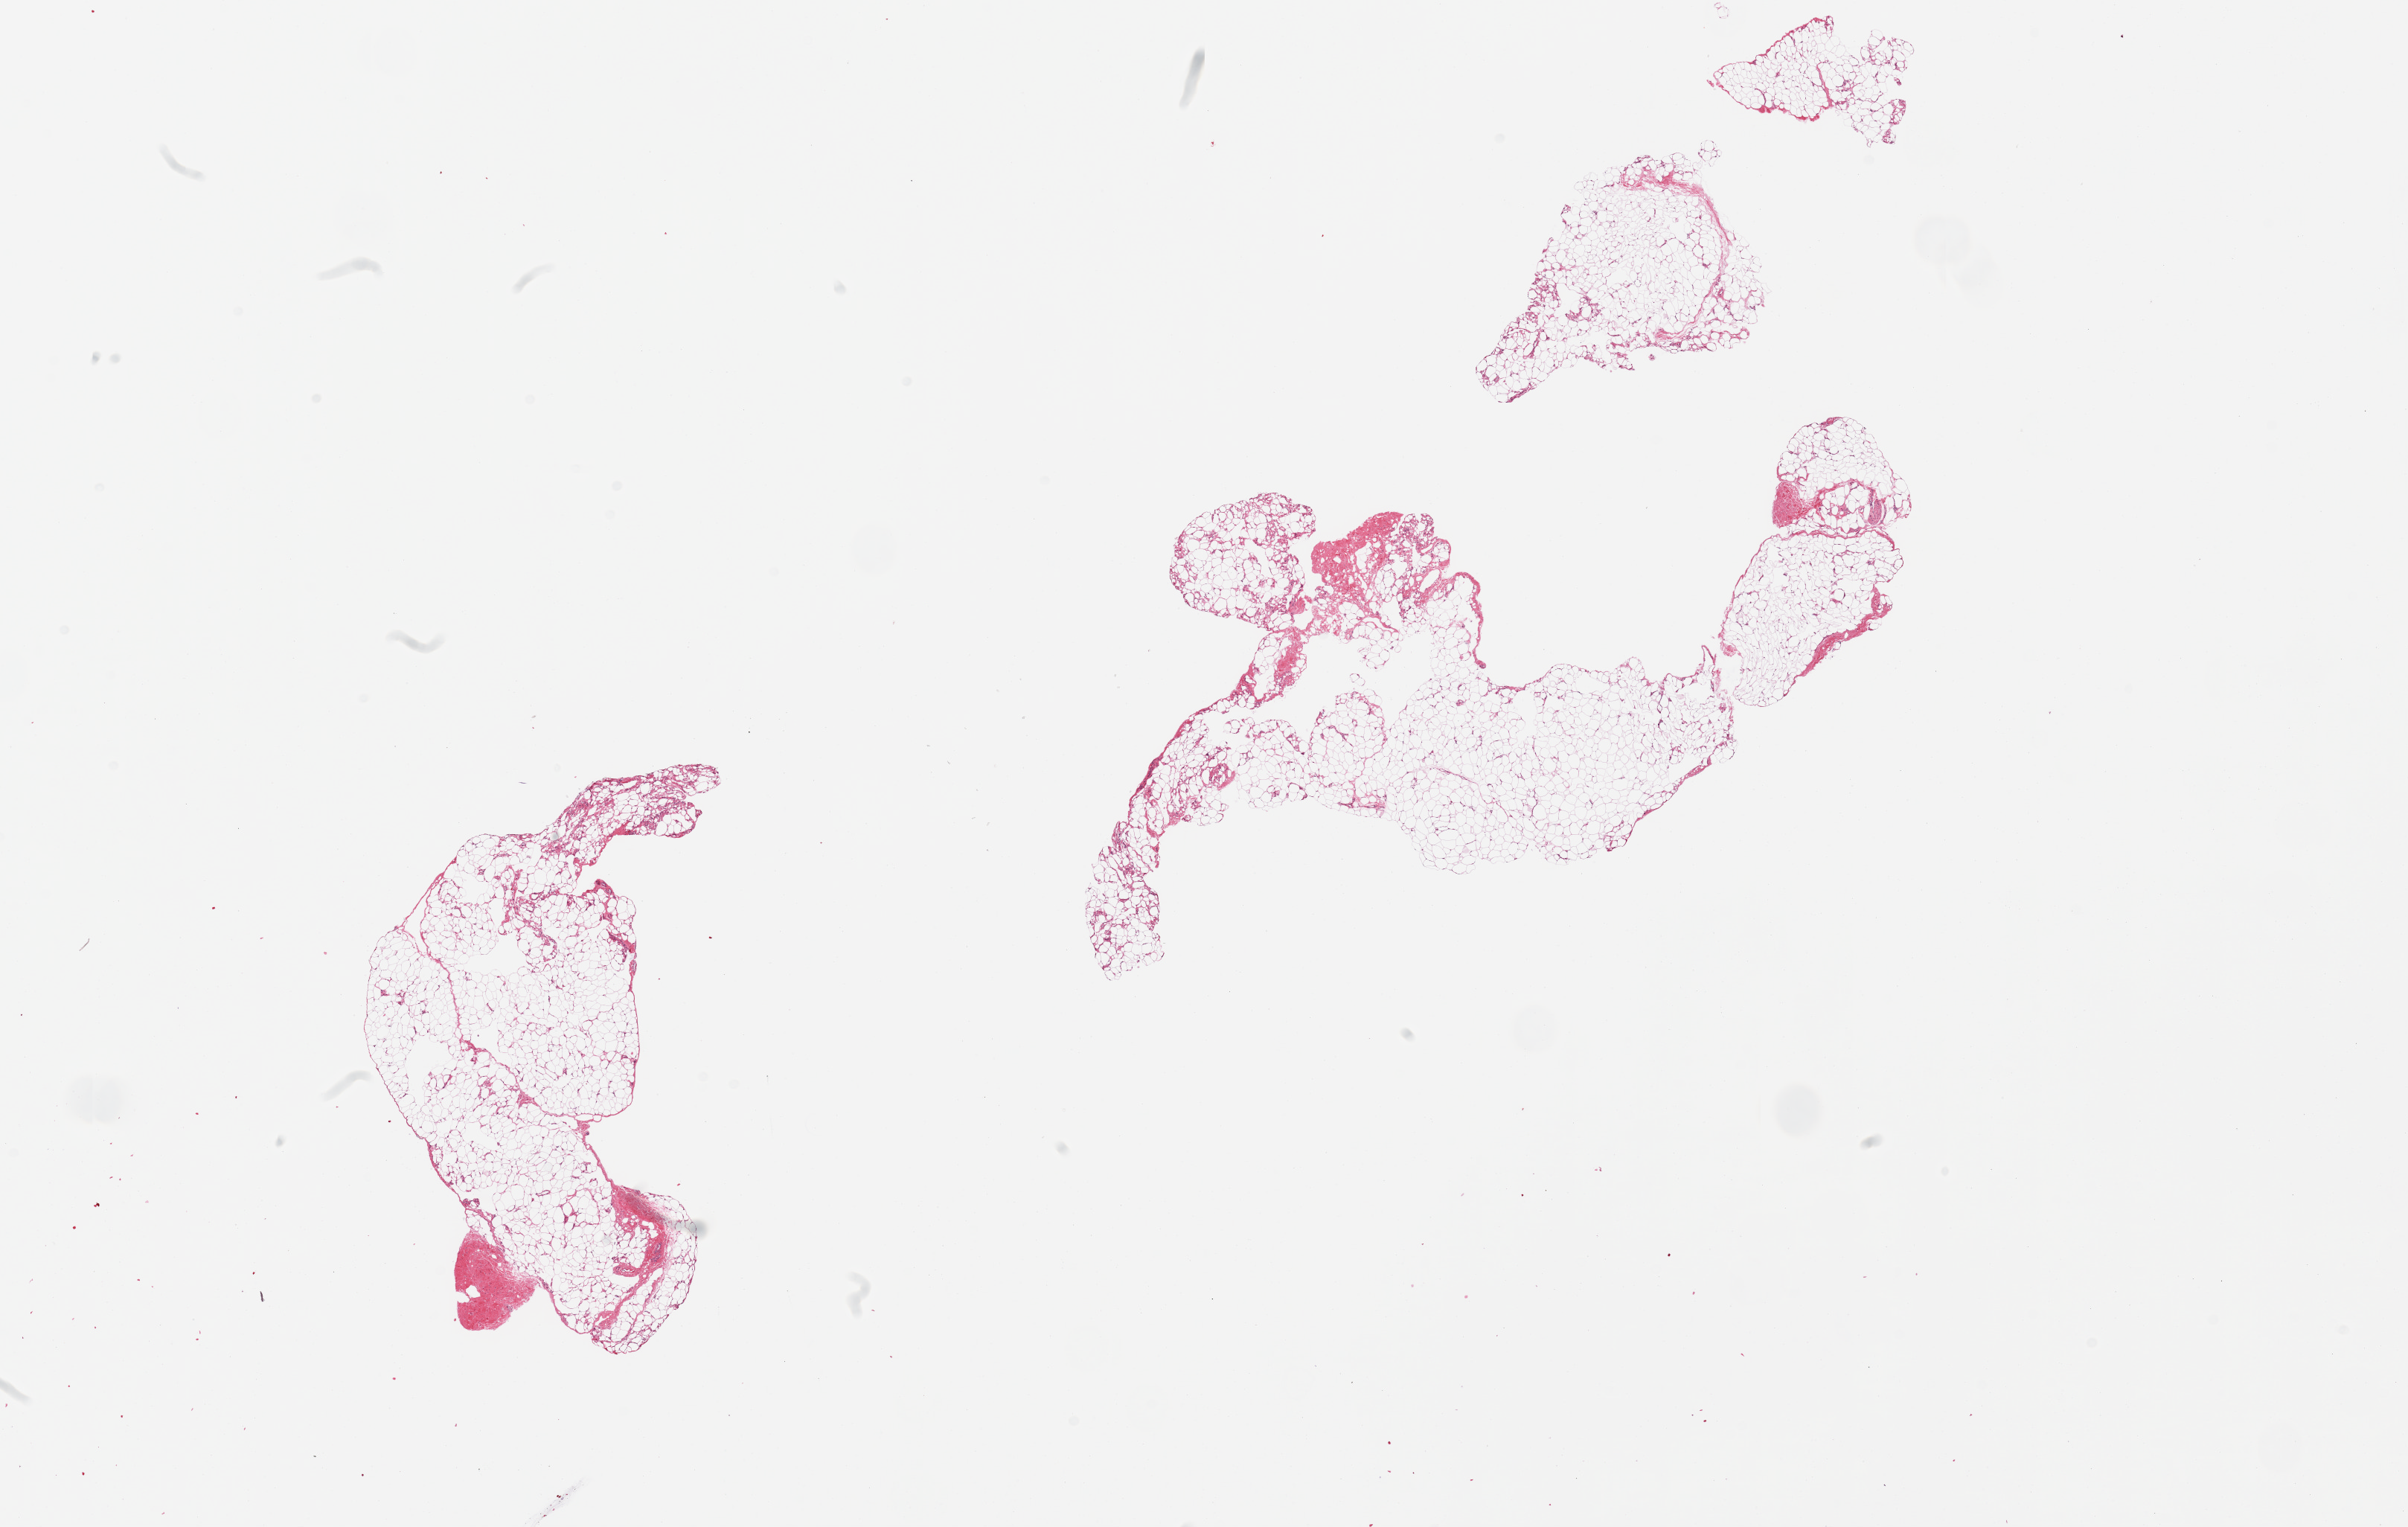
Digitized haematoxylin and eosin-stained section, brightfield, low-resolution overview of the scanned area, about 25.6 x 16.2 mm; PAXgene-fixed, paraffin-embedded tissue; target tissue: adipose tissue; donor tissue sample.
• pathologist's review note for this sample: 2 pieces (fragmented)